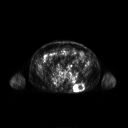
FDG PET of an extremity soft-tissue mass (from a PET/CT study), one axial slice. Position 89 of 267 along the scan axis. 128 × 128 image matrix. Male patient, age 61 years. Case-level facts recorded for this patient, not image findings: histological type: pleiomorphic leiomyosarcoma; grade: high; site of the primary tumour: left buttock.
Outlined on this slice (expert contour drawn on MRI and transferred to this co-registered scan by the dataset authors):
- gross tumour volume including surrounding oedema: bounding box [x1, y1, x2, y2] px = [73, 83, 84, 92]
- gross tumour volume (mass): [73, 84, 84, 92]